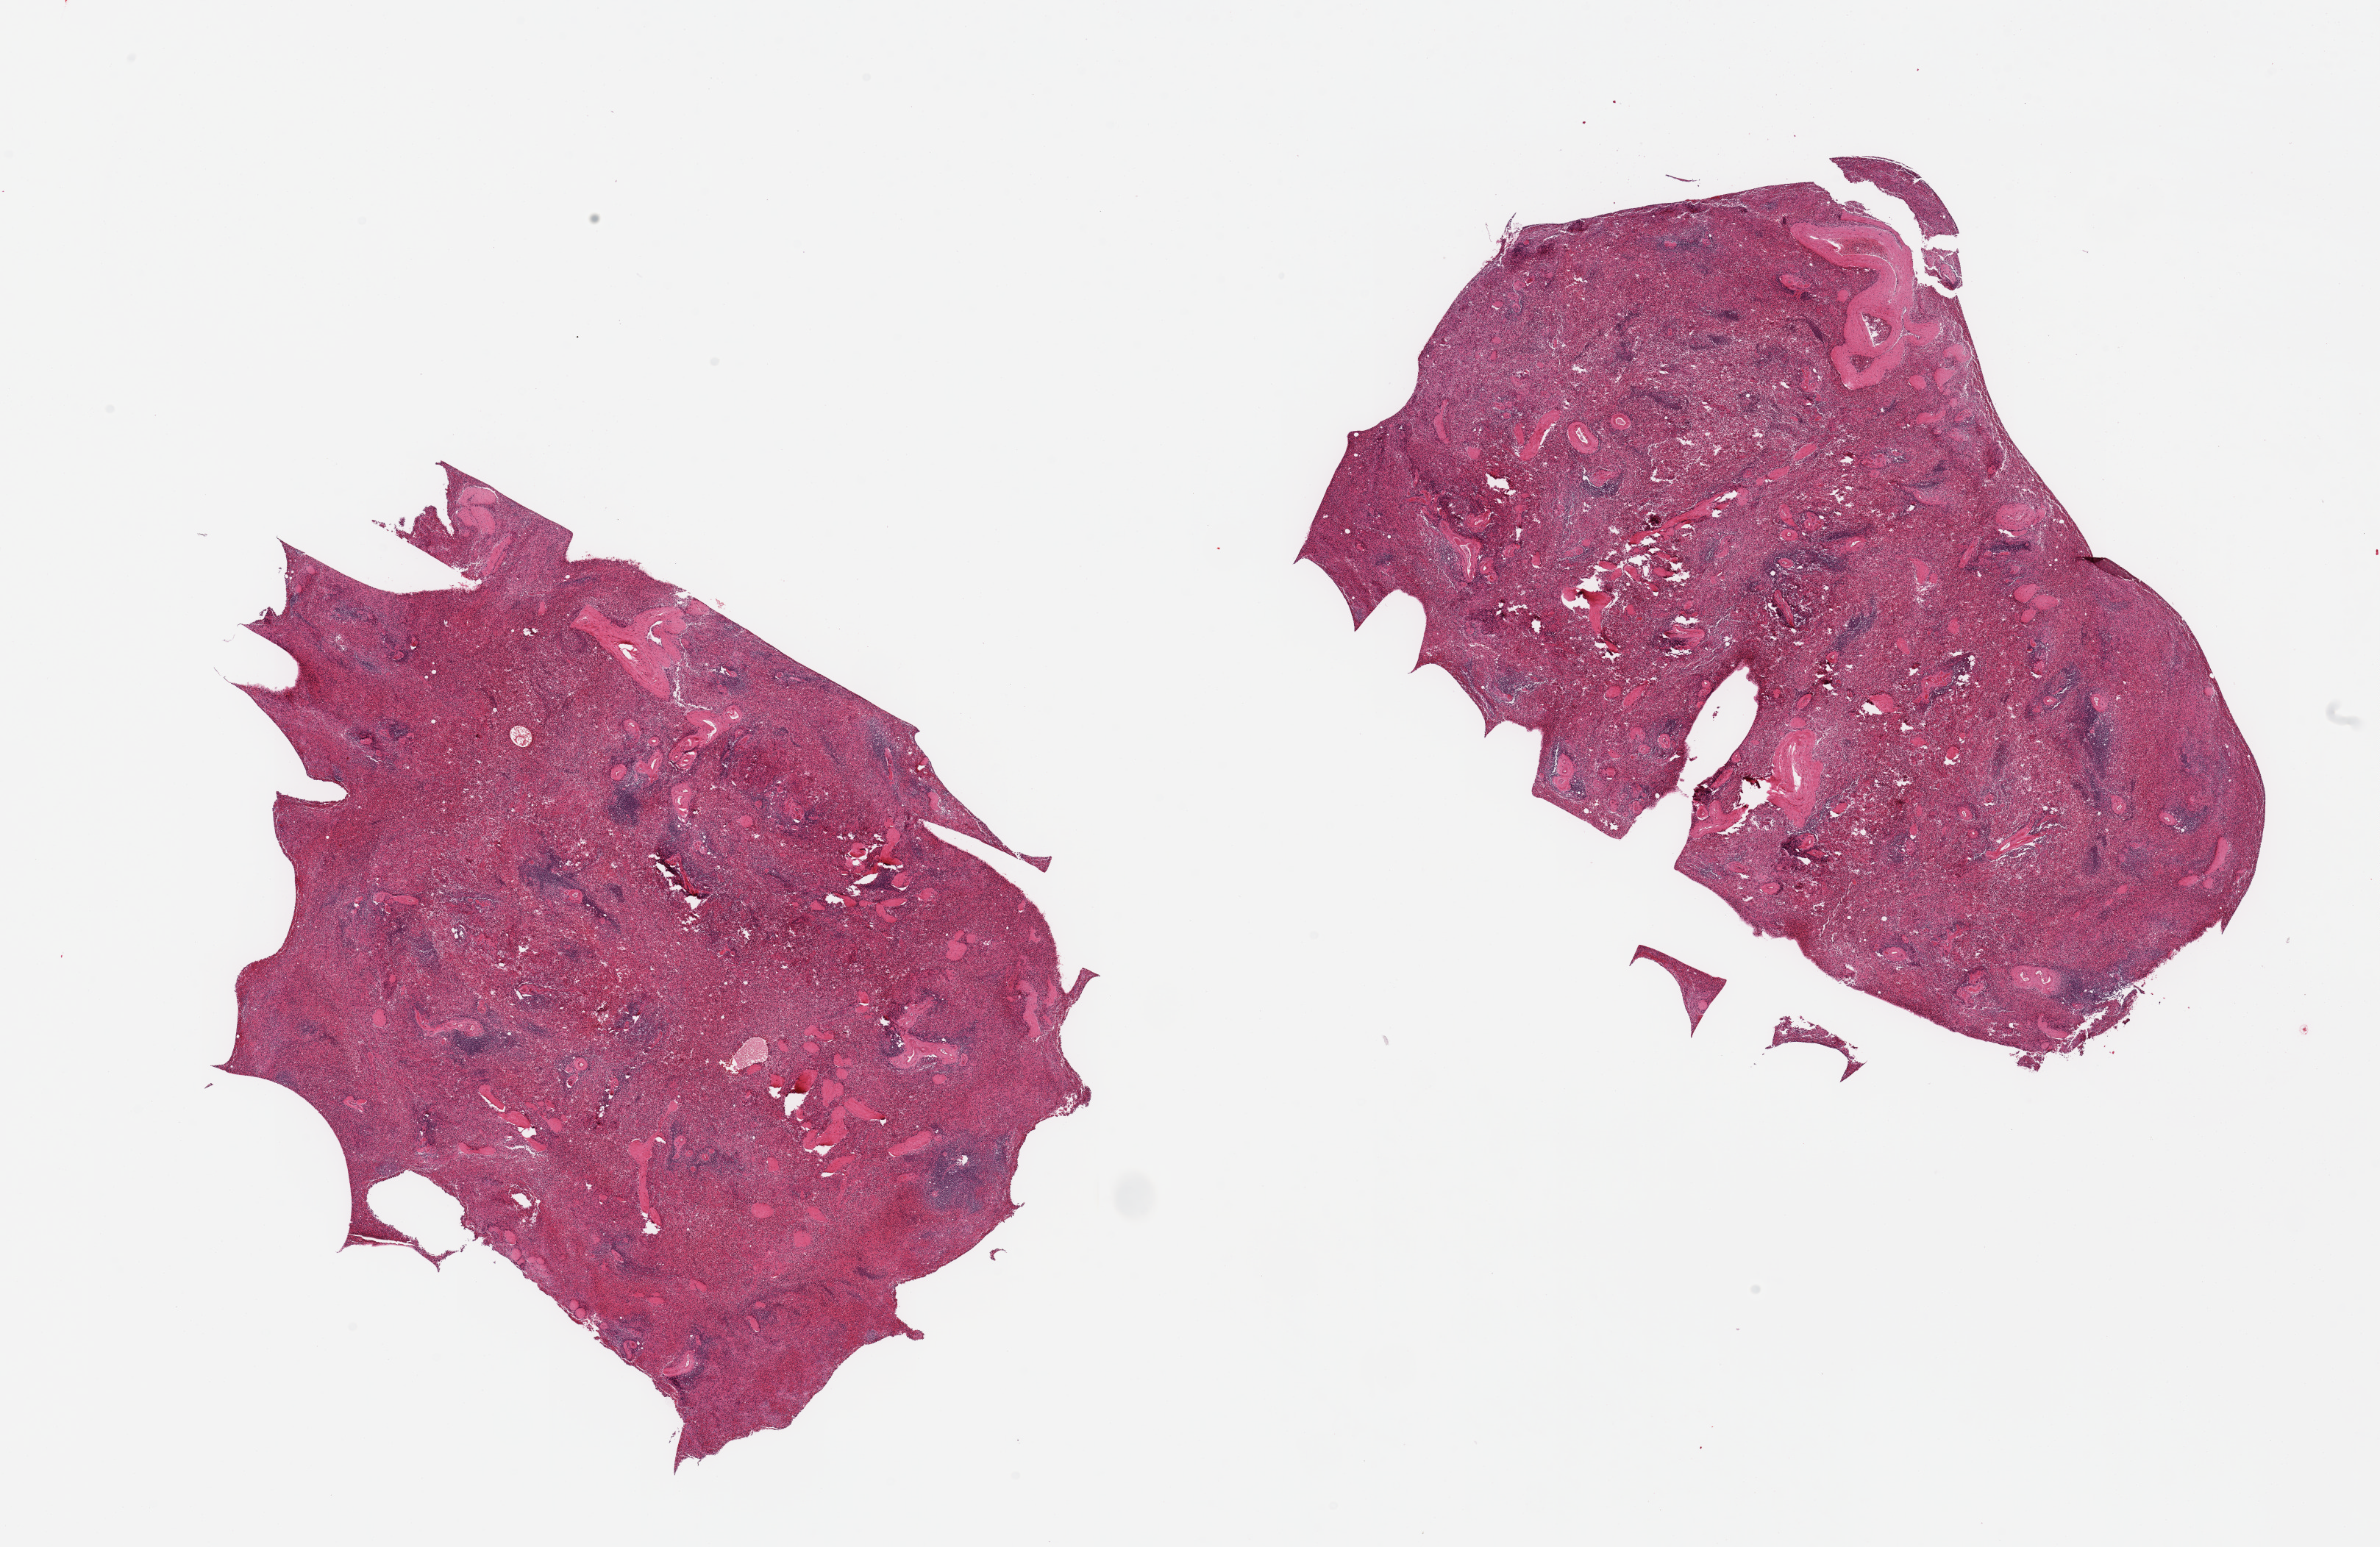
Digitized H&E-stained section — whole scanned area (about 25.6 x 16.6 mm, acquisition: 20x scan) shown as a low-resolution overview, PAXgene-fixed, paraffin-embedded tissue, section of spleen (target tissue), tissue donor sample. Male donor.
- reviewer comment on this tissue sample: 2 pieces, no abnormalities